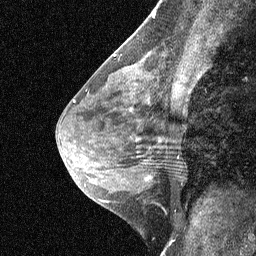
Breast MRI (dynamic contrast-enhanced), one sagittal slice. Position 34 of 64 along the scan axis. Dynamic contrast-enhanced study with each time point stored as its own series, time point 3 of 4 at this slice position (ordered by acquisition time). 1.5 T. TE 4.8 ms, TR 27 ms. 256 × 256 image matrix. Patient: female, 44 years. Case-level facts recorded for this patient, not image findings: setting: breast cancer imaged before/during neoadjuvant chemotherapy; receptor status: HR-positive, HER2-negative.
Structures marked on this image (semi-automatically segmented with operator editing):
- analysis volume of interest (the breast-tissue region the enhancement analysis was run in; not a lesion): bounding box (x1, y1, x2, y2) in pixels: (115, 117, 185, 188)
- tumour enhancement mask (voxels above the 90 % enhancement threshold inside the analysis volume of interest): (146, 177, 150, 180)